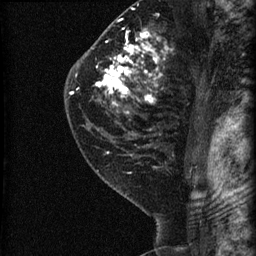
Breast MRI (dynamic contrast-enhanced), one sagittal slice. Position 46 of 60 along the scan axis. Dynamic contrast-enhanced series, image 2 of 3 at this slice position (ordered by acquisition). 1.5 T. TE 4.2 ms, TR 22.7 ms. 1.8 mm slice thickness. 256 × 256 image matrix, field of view 180 × 180 mm. Patient: female, 45 years. Case-level facts recorded for this patient, not image findings: setting: breast cancer imaged before/during neoadjuvant chemotherapy; receptor status: HR-positive, HER2-negative.
Outlined on this slice (semi-automatic segmentation, software-assisted and operator-edited):
- analysis volume of interest (the breast-tissue region the enhancement analysis was run in; not a lesion): bounding box [x1, y1, x2, y2] px = [74, 11, 205, 140]
- tumour enhancement mask (voxels above the 90 % enhancement threshold inside the analysis volume of interest): [96, 30, 165, 104]